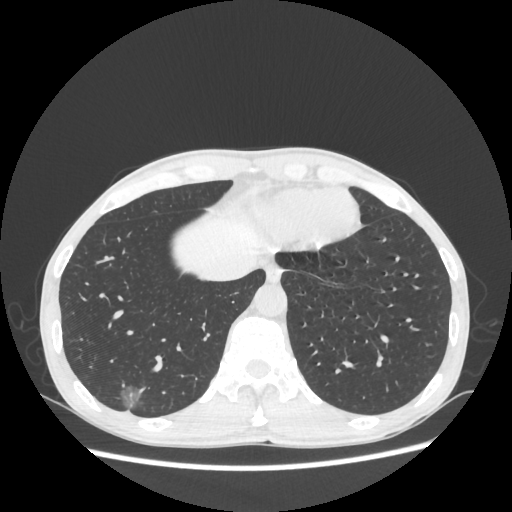
Chest CT, one axial slice; position 67 of 270 along the scan axis; reconstruction kernel STANDARD; lung window (W 1500 / L -600 HU); 512 × 512 image matrix, field of view 360 × 360 mm. Male patient, age 60 years. Case-level facts recorded for this patient, not image findings: clinical TNM (as recorded): T1c N0 M0.
Annotated regions visible in this slice (bounding box drawn by a radiologist):
- lung tumour (recorded histology: adenocarcinoma): bounding box (x1, y1, x2, y2) in pixels: (113, 379, 151, 421)